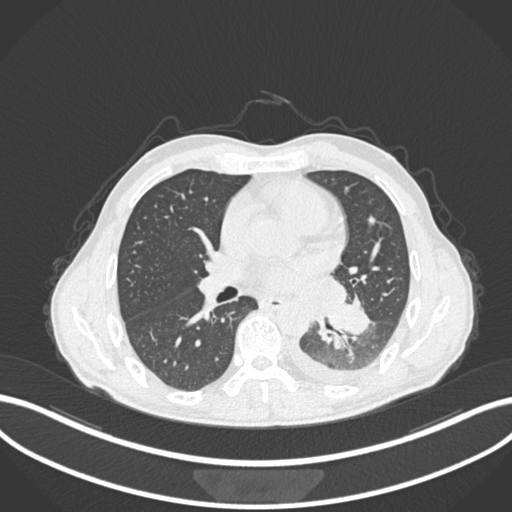
Chest CT, one axial slice. Position 123 of 222 along the scan axis. Reconstruction kernel B30f. 120 kVp. Lung window (W 1500 / L -600 HU). 1 mm slice thickness. 512 × 512 image matrix, field of view 400 × 400 mm. Patient: male, 47 years. Case-level facts recorded for this patient, not image findings: clinical TNM (as recorded): T3 N1 M1c.
Annotated regions visible in this slice (bounding box drawn by a radiologist):
- lung tumour (recorded histology: small cell carcinoma): bounding box [x1, y1, x2, y2] px = [328, 295, 371, 337]